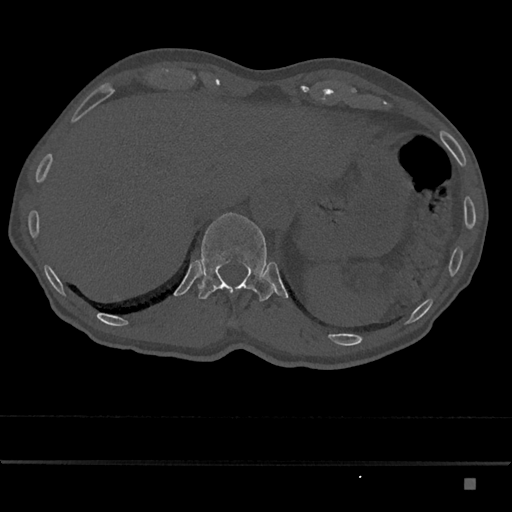
CT including the spine, one axial slice; slice 622 of 797 in the series (ordered by position); reconstruction kernel Br40s/3; bone window (W 1800 / L 400 HU); 0.5 mm slice thickness; 512 × 512 image matrix, field of view 390 × 390 mm. Patient: male, 72 years. Case-level facts recorded for this patient, not image findings: primary cancer: prostate.
Annotated regions visible in this slice (semi-automatic segmentation, software-assisted and operator-edited):
- T12 vertebra: box from (x=198, y=212) to (x=275, y=301) px